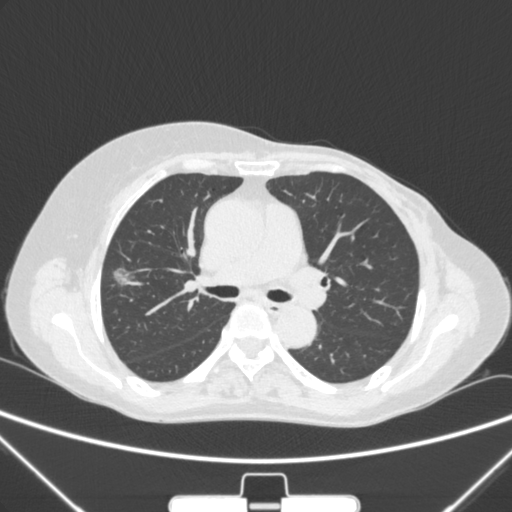
Chest CT, one axial slice. Slice 156 of 265 in the series (ordered by position). 120 kVp. Lung window (W 1500 / L -600 HU). 1 mm slice thickness. 512 × 512 image matrix. Female patient, age 64 years. Case-level facts recorded for this patient, not image findings: clinical TNM (as recorded): T1c N0 M0; histopathological grade: G1-2.
Annotated regions visible in this slice (bounding box drawn by a radiologist):
- lung tumour (recorded histology: adenocarcinoma): bounding box <98,256,137,287> (left, top, right, bottom; pixels)